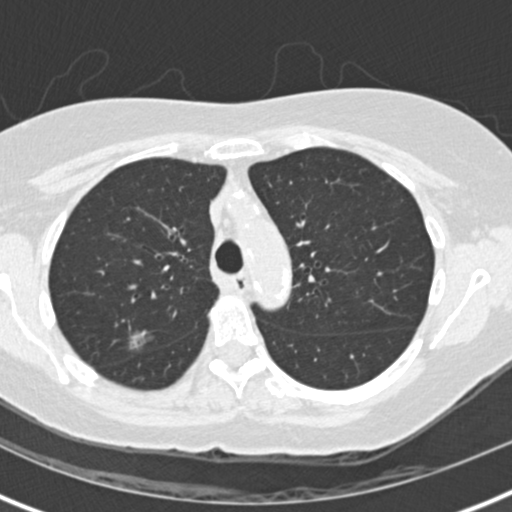
Low-dose screening chest CT, one axial slice; position 102 of 147 along the scan axis; reconstruction kernel B30f; lung window (W 1500 / L -600 HU); 512 × 512 image matrix.
Outlined on this slice (outlined manually by an expert reader):
- lesion 1 (tumor, upper lobe of right lung): bounding box (x1, y1, x2, y2) in pixels: (128, 330, 147, 349)